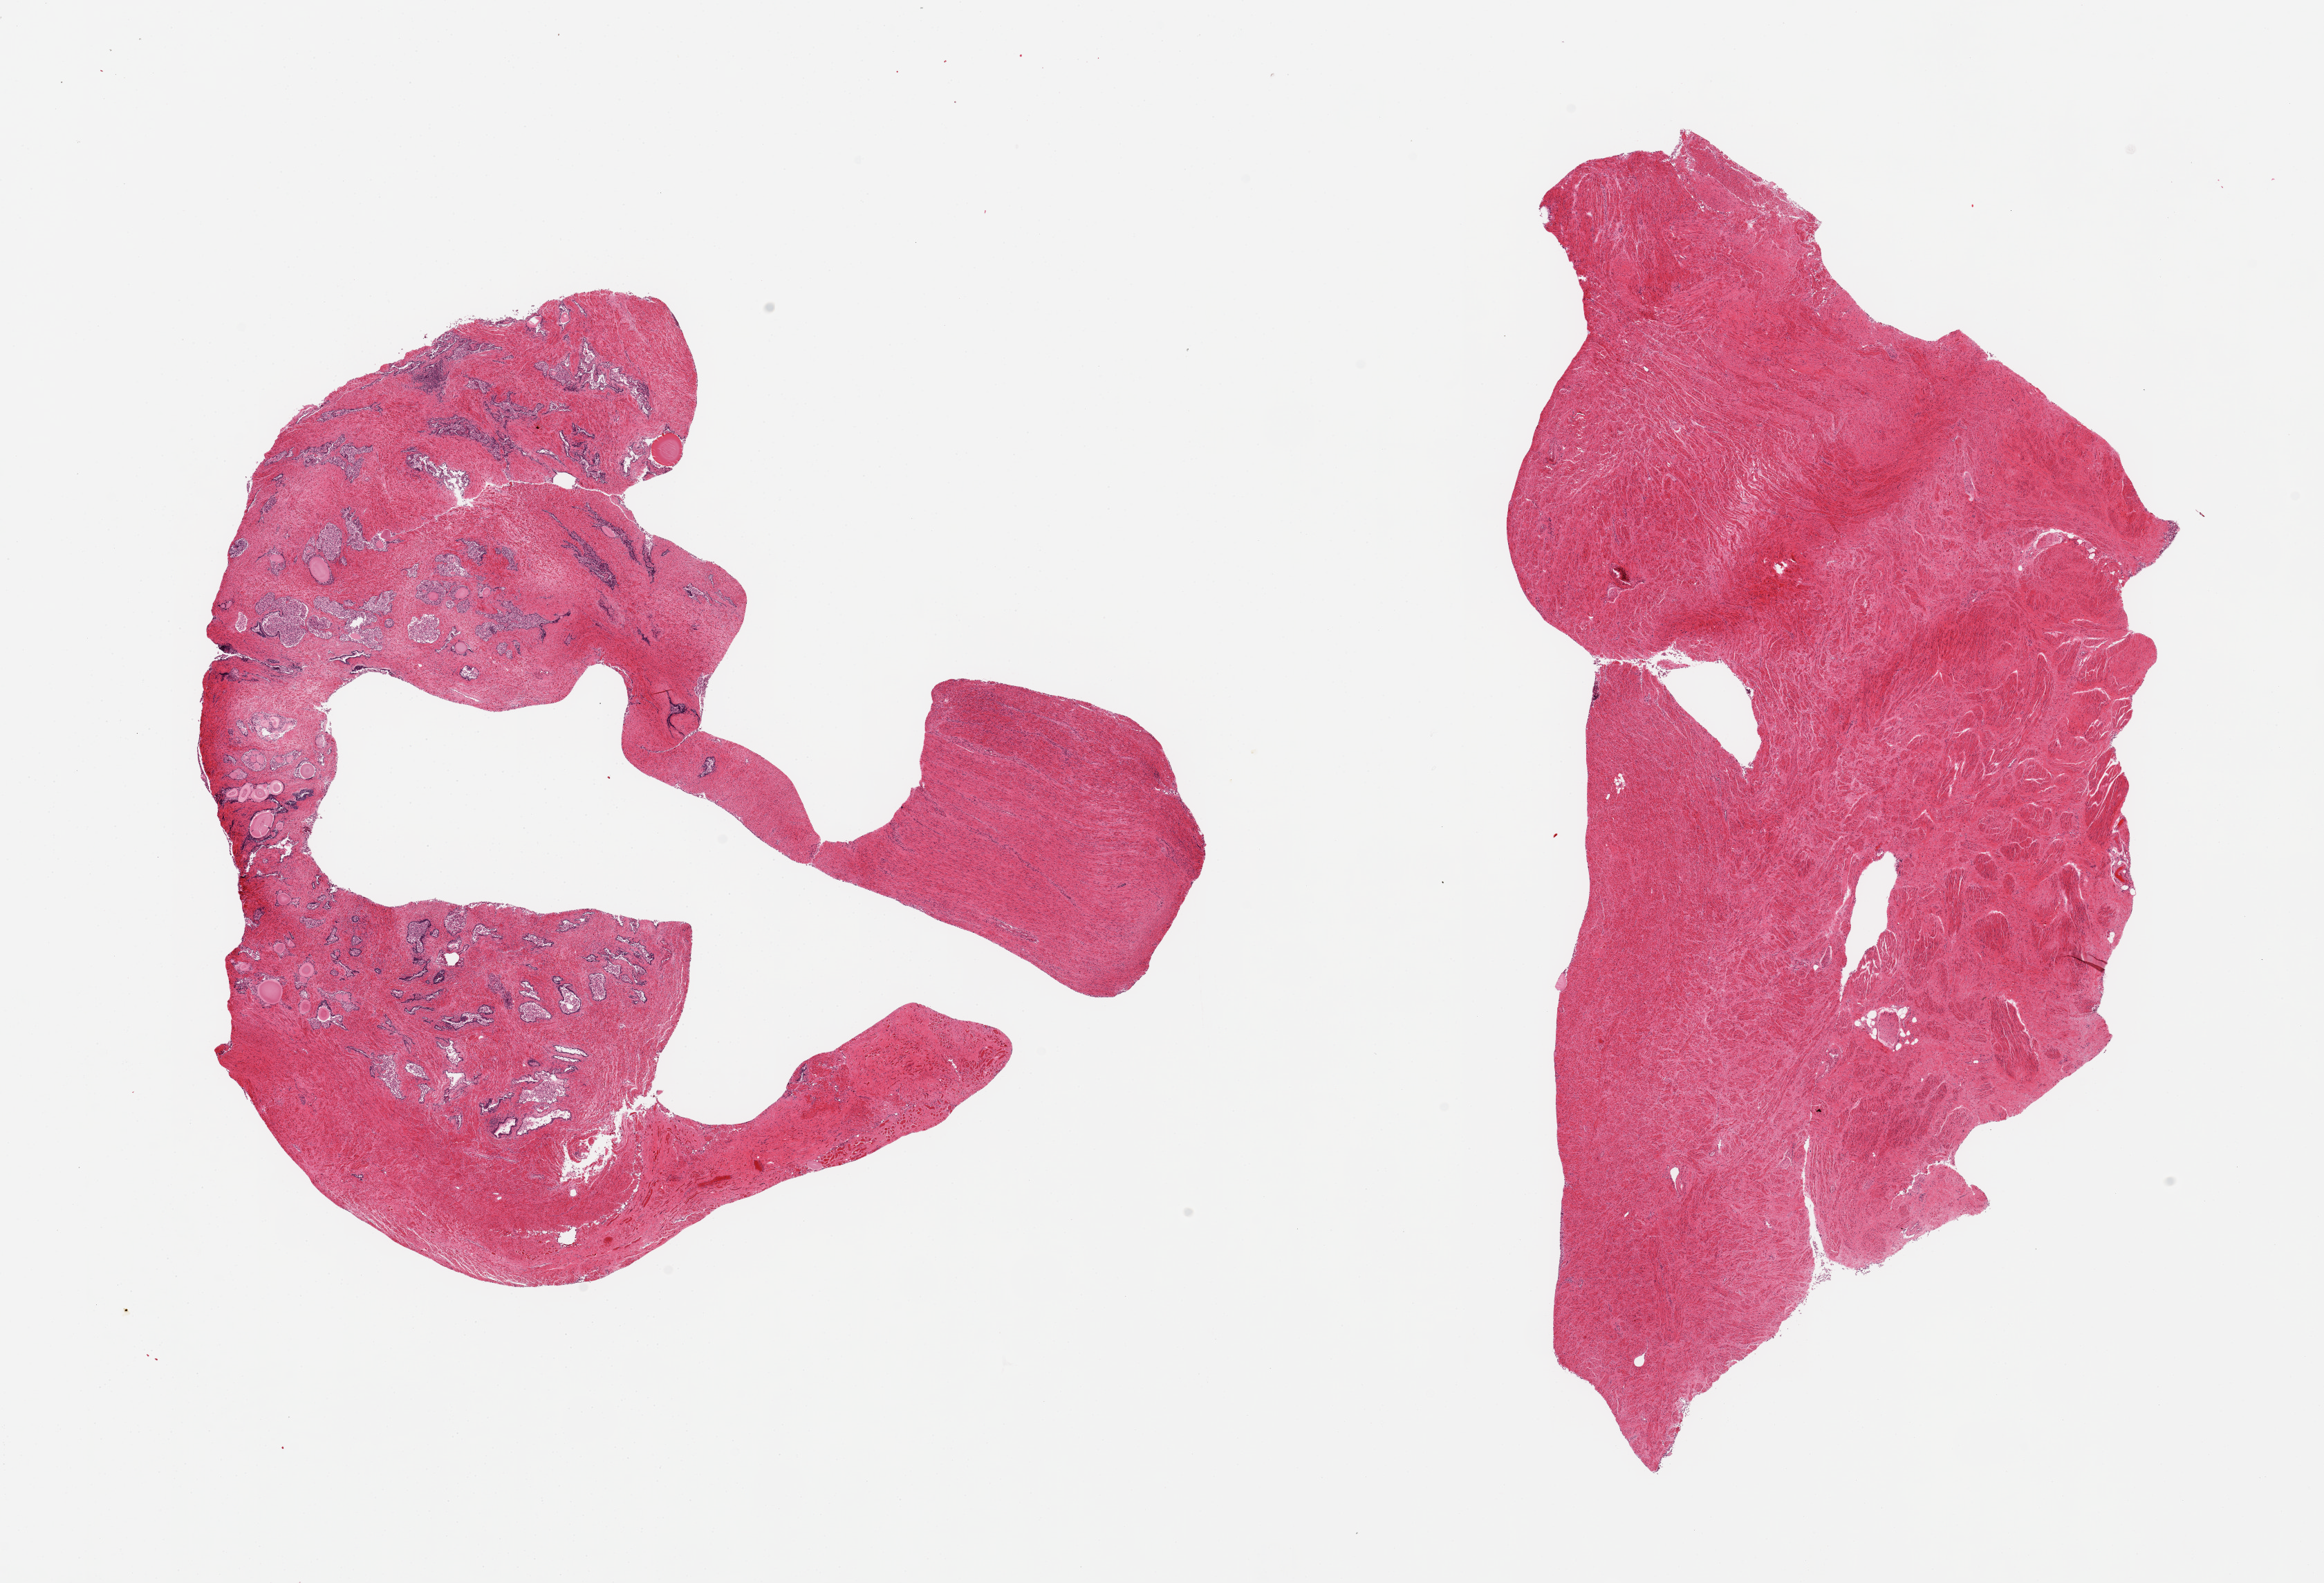
Digitized hematoxylin and eosin (H&E)-stained section — a low-resolution overview of the entire scanned area, about 26.6 x 18.1 mm (from a 20x scan); PAXgene-fixed paraffin-embedded (PFPE) section; sampled site (target tissue): prostate; donor tissue sample.
Reviewer comment on this tissue sample: 2 pieces; 1 piece has autolyzed glands and preserved fibromuscular stroma; other is all fibromuscular stroma.